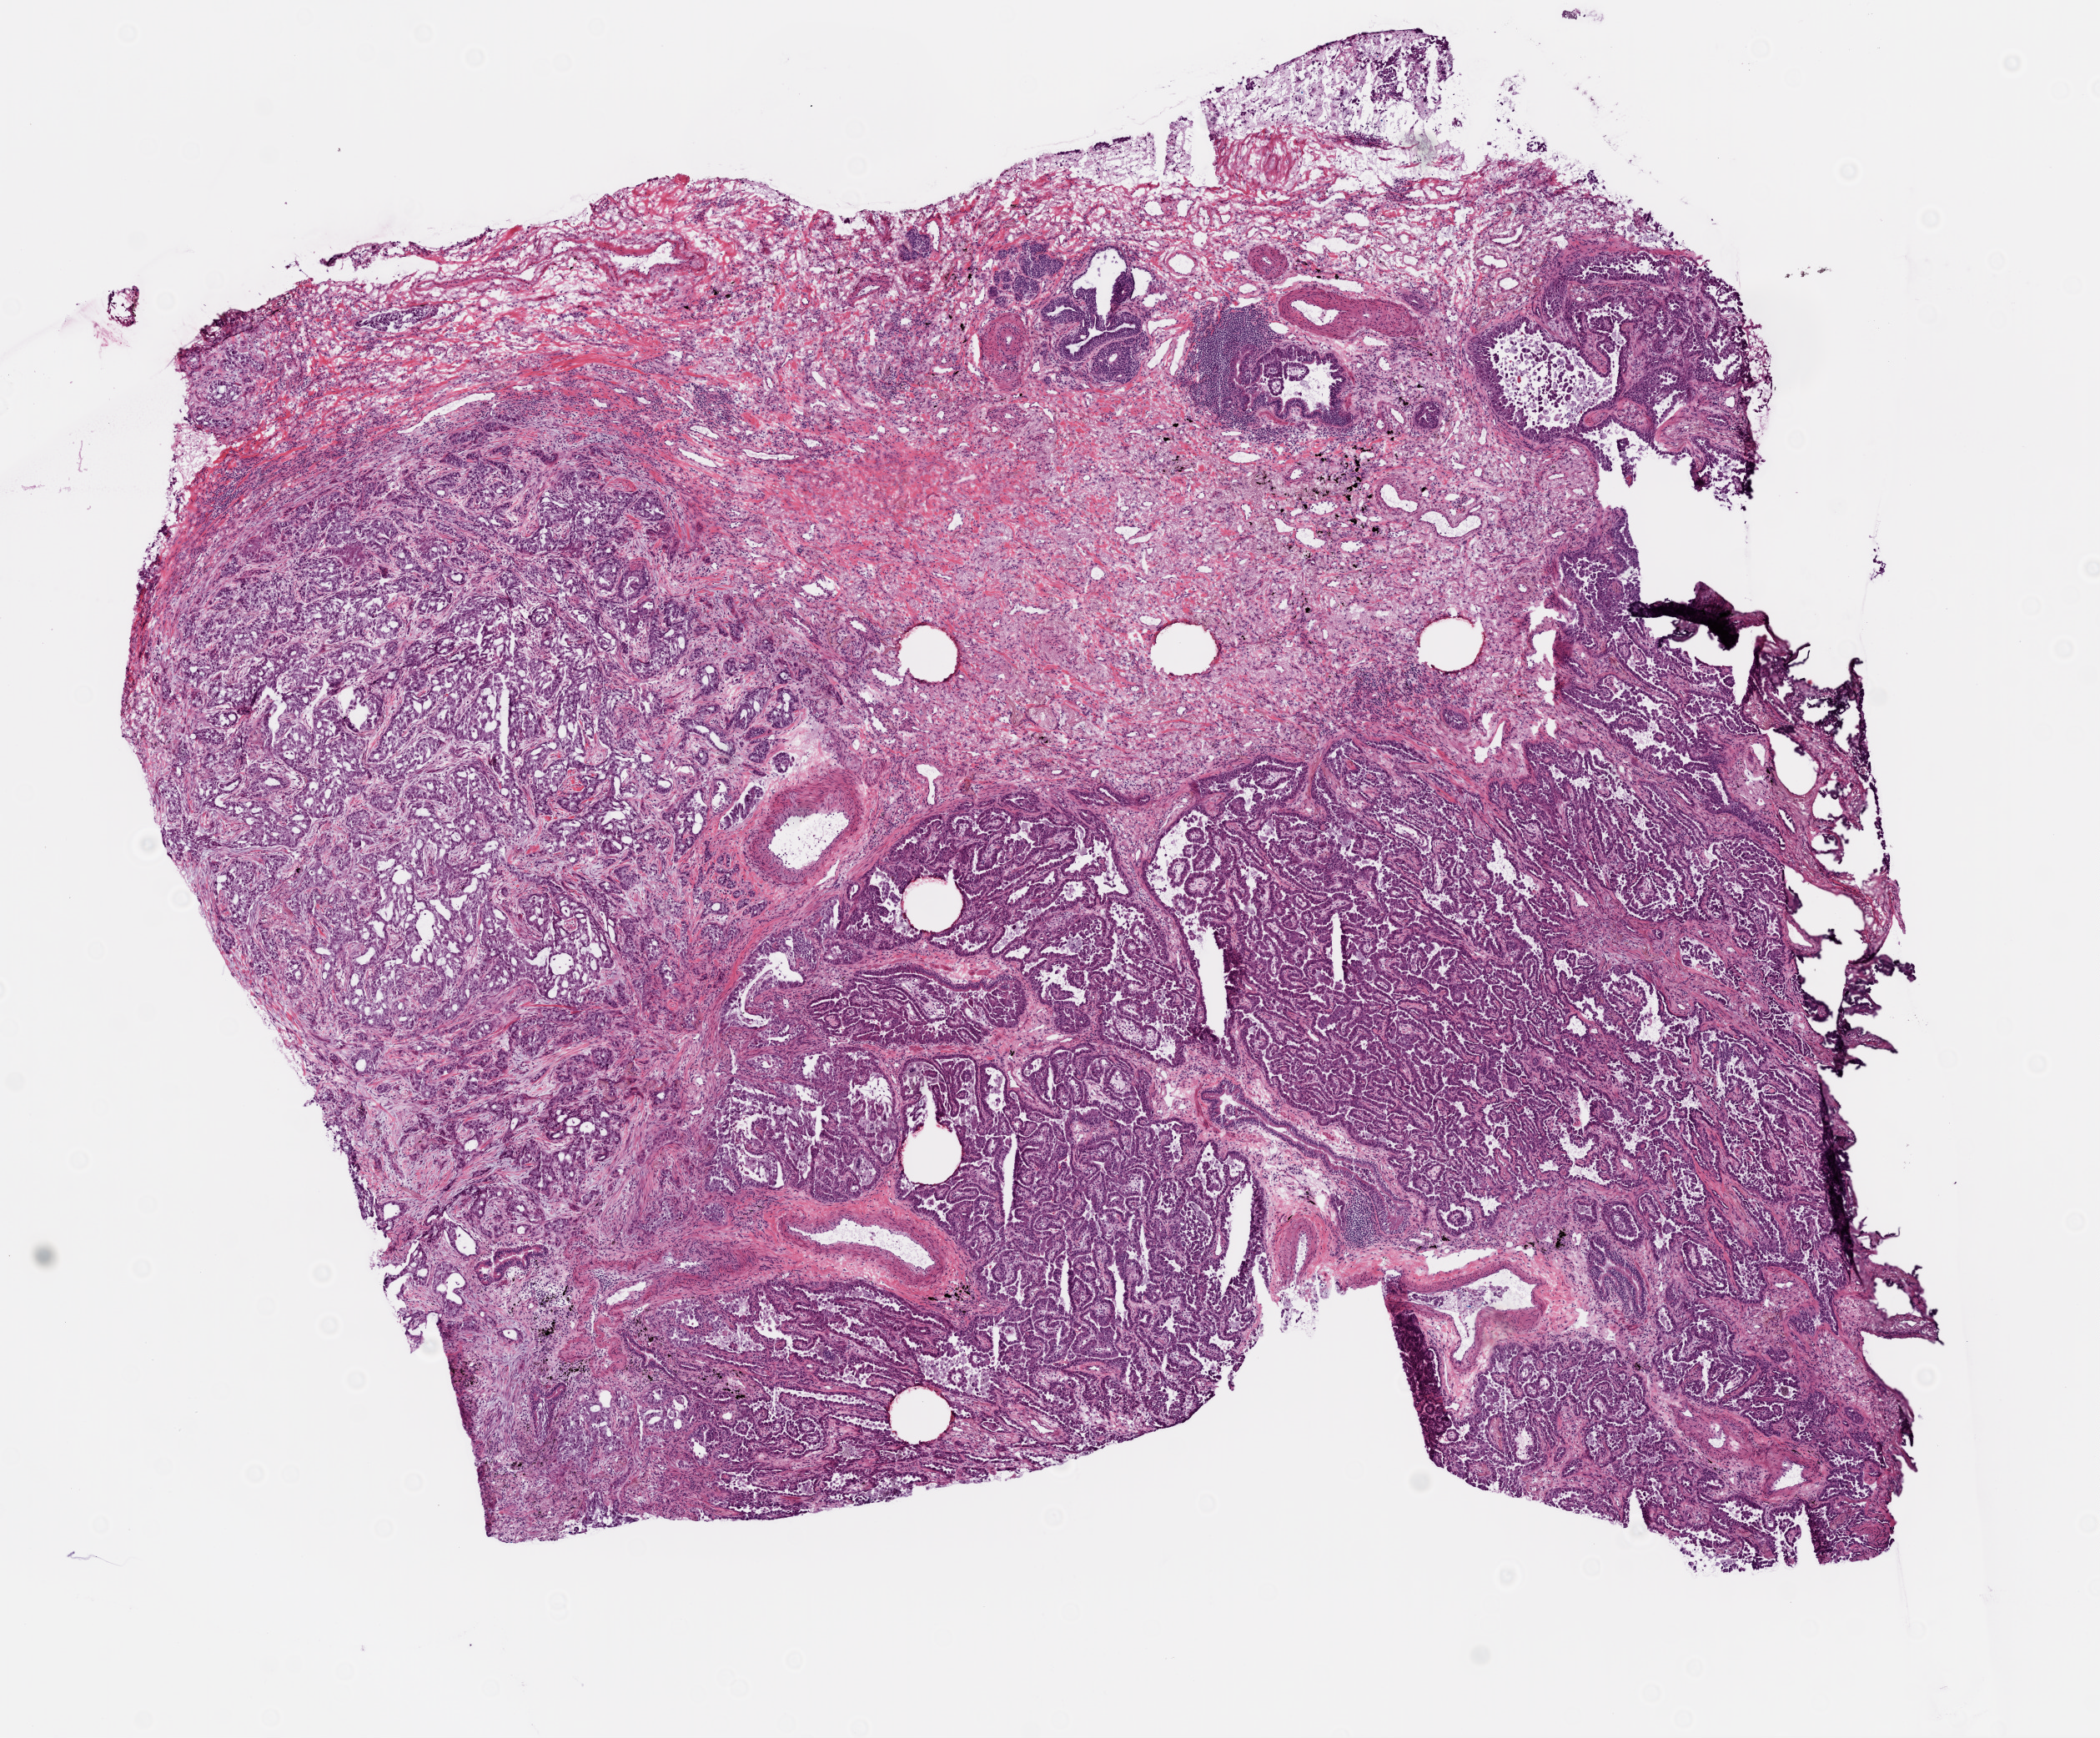
Digitized H&E-stained tissue section (whole slide) — a low-resolution overview of the entire scanned area, about 10.2 x 8.4 mm. Frozen section. Sample: primary tumour, lung. Male patient; age at initial diagnosis 64 years. Pathologist review of this section (percent, as recorded): tumour cells 100%, tumour nuclei 85%, necrosis 0%. Inflammatory infiltration, as recorded: monocyte infiltration 5%.
* pathologic diagnosis: Adenocarcinoma with mixed subtypes
* AJCC pathologic stage: IB (7th edition)